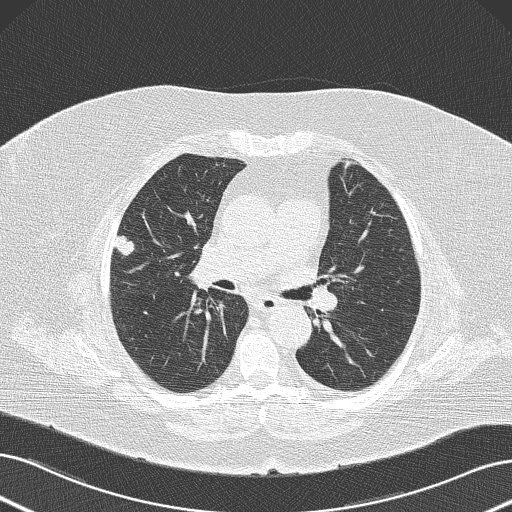
Low-dose screening chest CT, one axial slice; slice 79 of 145 in the series (ordered by position); lung window (W 1500 / L -600 HU); 512 × 512 image matrix, field of view 364 × 364 mm.
Structures marked on this image (expert manual segmentation):
- lesion 1 (tumor, upper lobe of right lung): box from (x=113, y=235) to (x=135, y=258) px